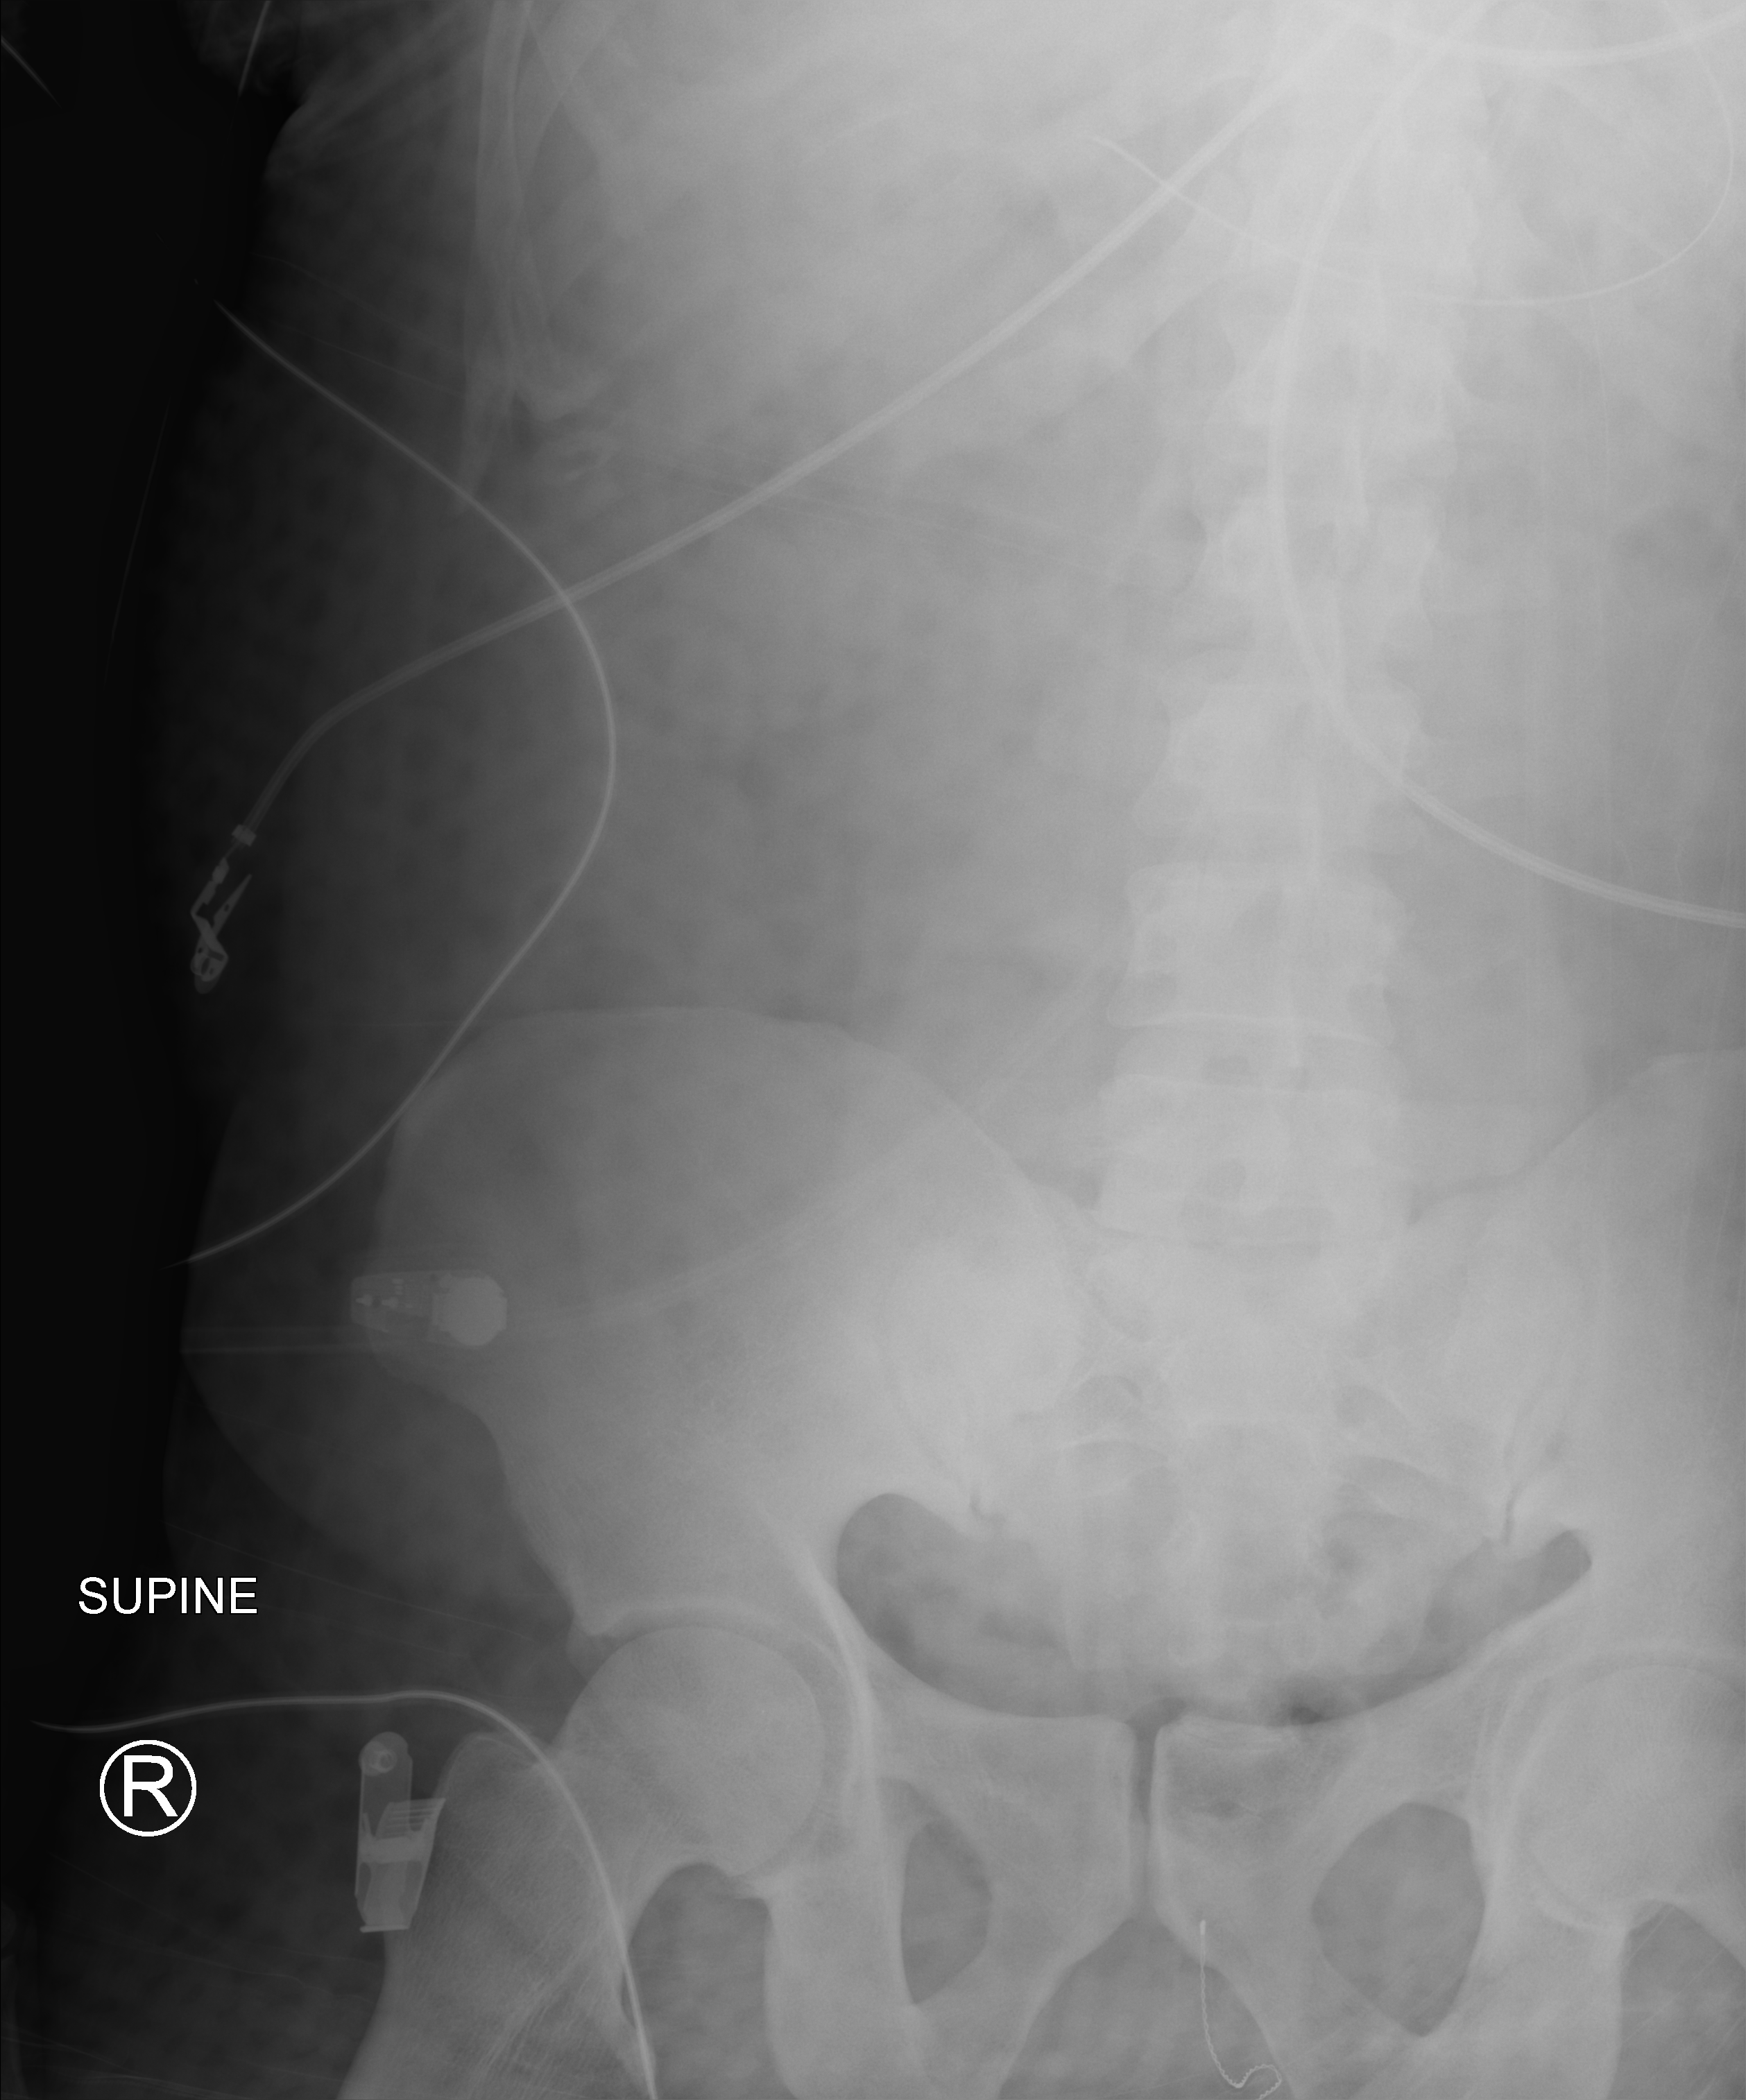
Bedside abdomen radiograph (computed radiography); anteroposterior (AP) projection. Patient hospitalised with COVID-19; male, aged 18–59 years.
Hospital-stay facts (about this admission, not read from this image; timing relative to this image not recorded): admitted to intensive care during this hospital stay: yes.